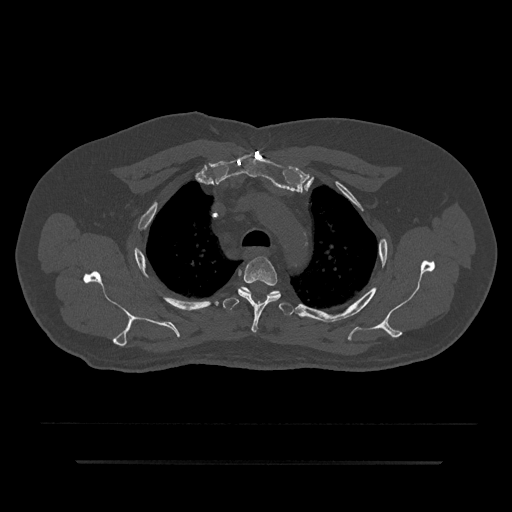
CT including the spine, one axial slice; slice 647 of 797 in the series (ordered by position); 120 kVp; bone window (W 1800 / L 400 HU); 512 × 512 image matrix, field of view 464 × 464 mm. Patient: male, 59 years. Case-level facts recorded for this patient, not image findings: primary cancer: bile ducts; vertebrae with lytic lesions (as recorded): T10.
Annotated regions visible in this slice (semi-automatic segmentation, software-assisted and operator-edited):
- T3 vertebra: box from (x=238, y=256) to (x=281, y=333) px
- T4 vertebra: (x=223, y=287)–(x=295, y=316)